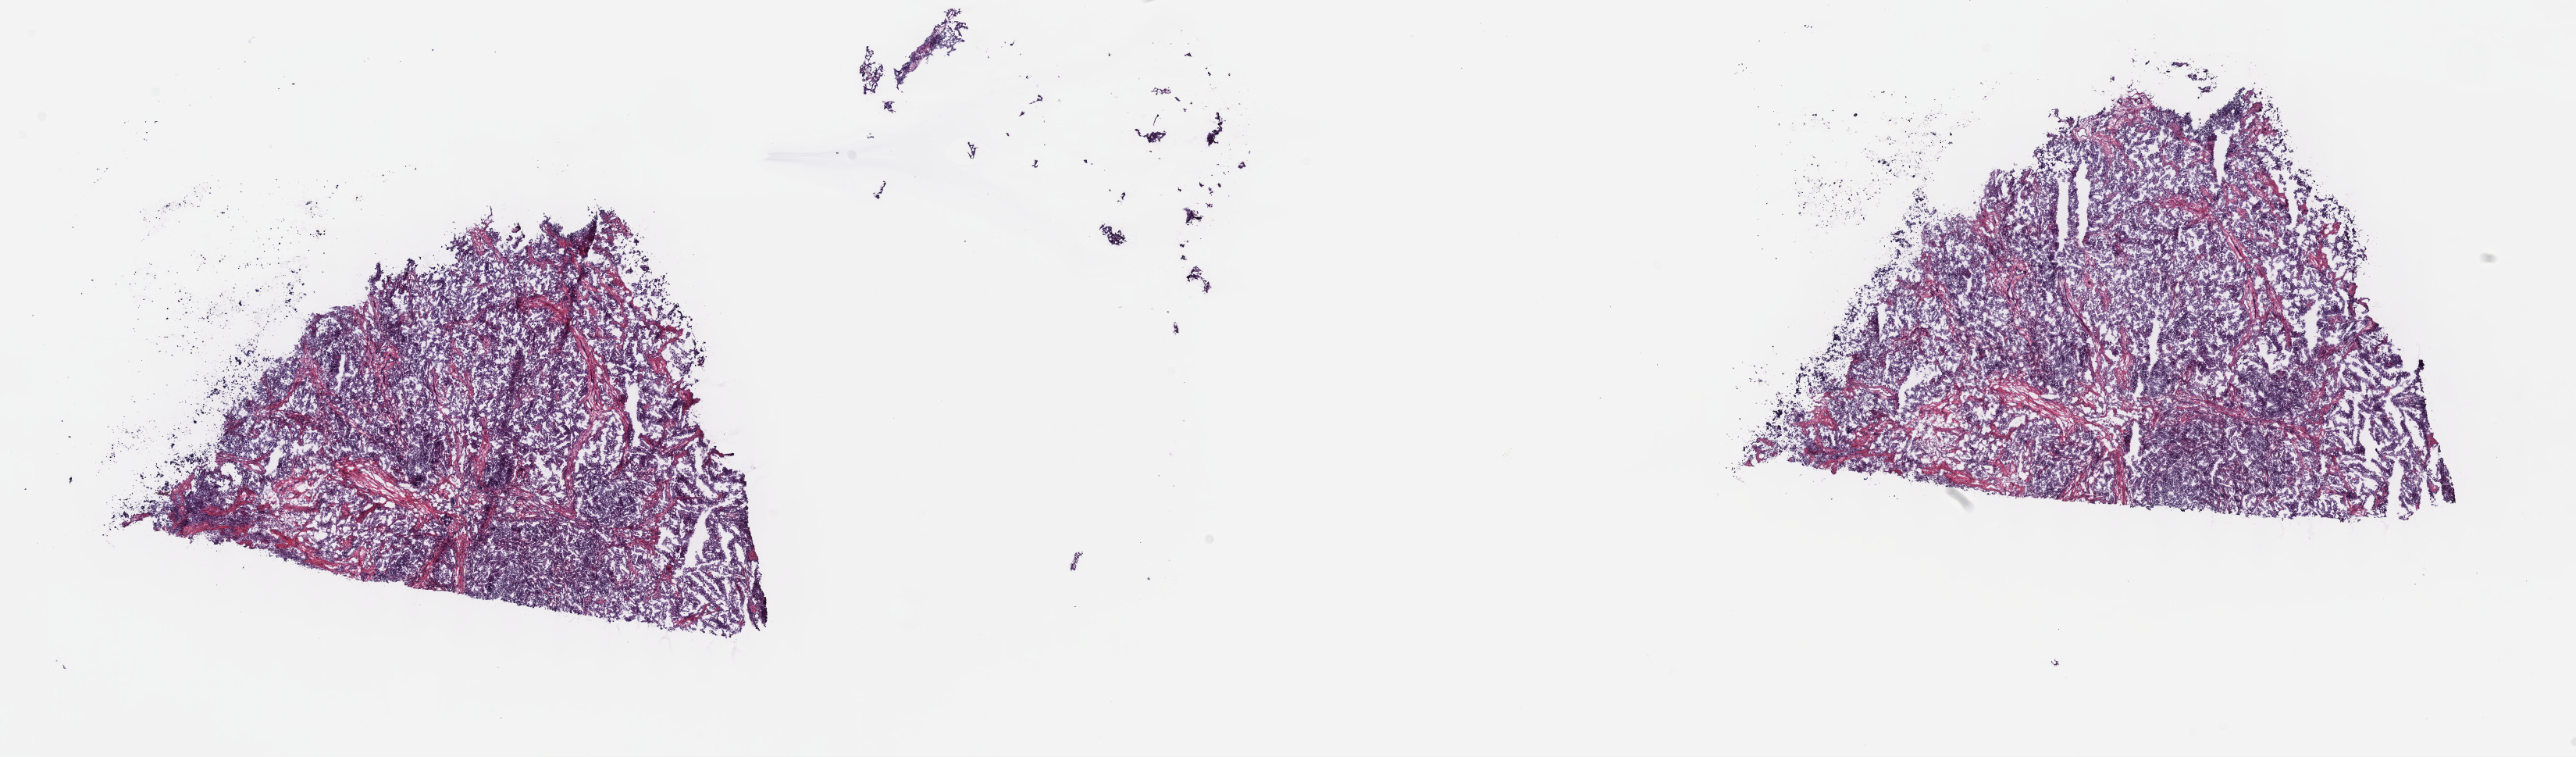
Whole-slide histology image, H&E — shown as a low-resolution overview of the whole scanned area (about 26.7 x 7.8 mm, from a 40x scan), frozen section from the top of the tissue portion, sample: primary tumour, testis. Male patient; age at initial diagnosis 31 years. Pathologist review of this section (percent, as recorded): tumour cells 100%, tumour nuclei 75%, normal cells 0%, stromal cells 0%, necrosis 0%. Inflammatory infiltration, as recorded: lymphocyte infiltration 0%, monocyte infiltration 0%, neutrophil infiltration 0%.
* diagnosis: Seminoma, NOS
* laterality: right
* AJCC pathologic stage: IA (7th edition)